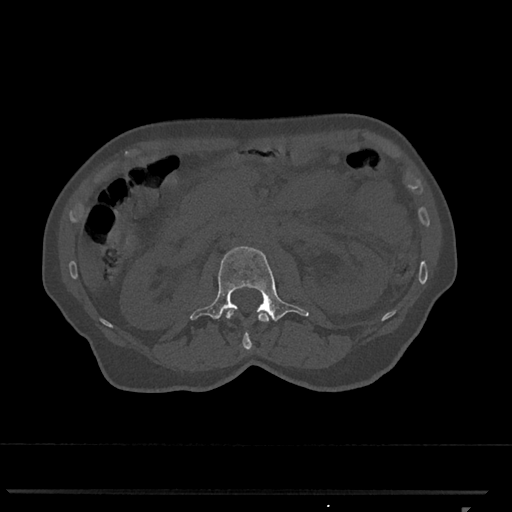
CT including the spine, one axial slice. Slice 353 of 793 in the series (ordered by position). Bone window (W 1800 / L 400 HU). 512 × 512 image matrix, field of view 380 × 380 mm. Female patient, age 62 years. From the clinical record (not read from this slice): primary cancer: renal.
Structures marked on this image (semi-automatically segmented with operator editing):
- L1 vertebra: bounding box (x1, y1, x2, y2) in pixels: (226, 309, 269, 349)
- L2 vertebra: (190, 246, 309, 322)